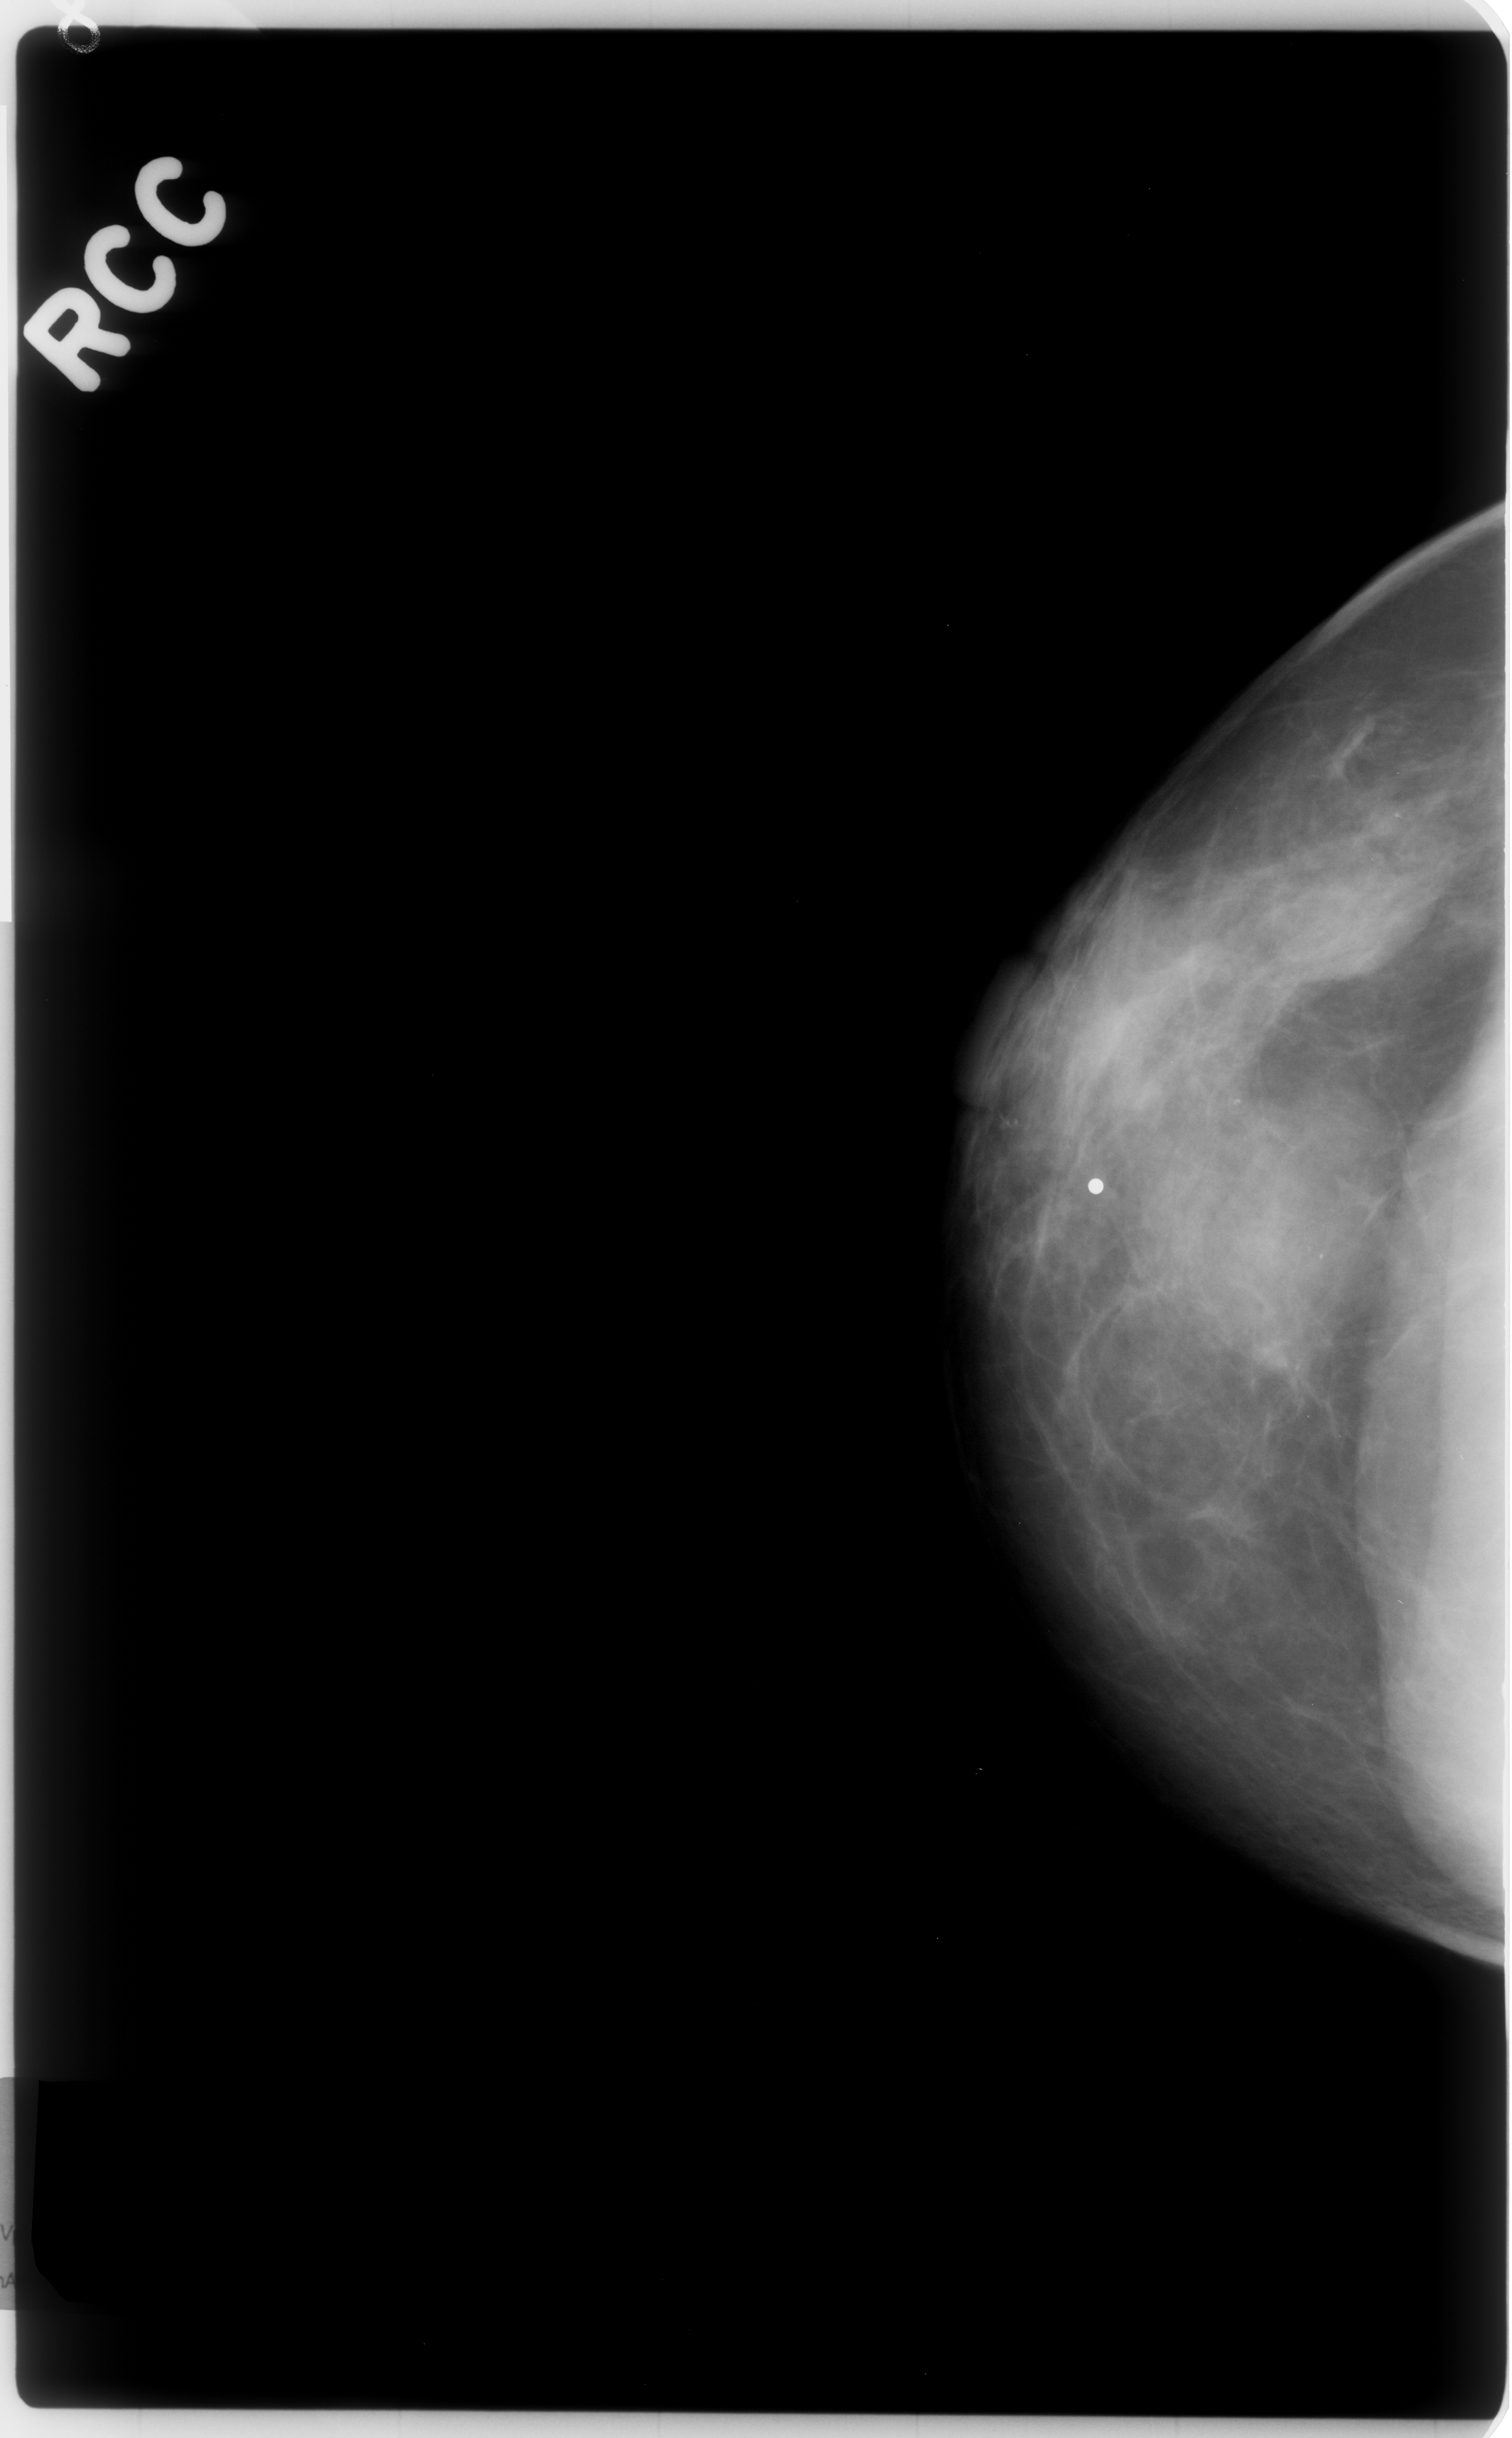
Mammogram (digitized film). Right breast. Craniocaudal (CC) view. Breast composition: scattered fibroglandular densities (BI-RADS density category 2 of 4). 1512 × 2438 image matrix.
Marked abnormalities (boxes around the expert regions of interest):
- mass, shape oval, margins obscured; BI-RADS assessment category 3; pathology result (as recorded, not read from the image): benign: box from (x=1285, y=804) to (x=1443, y=983) px